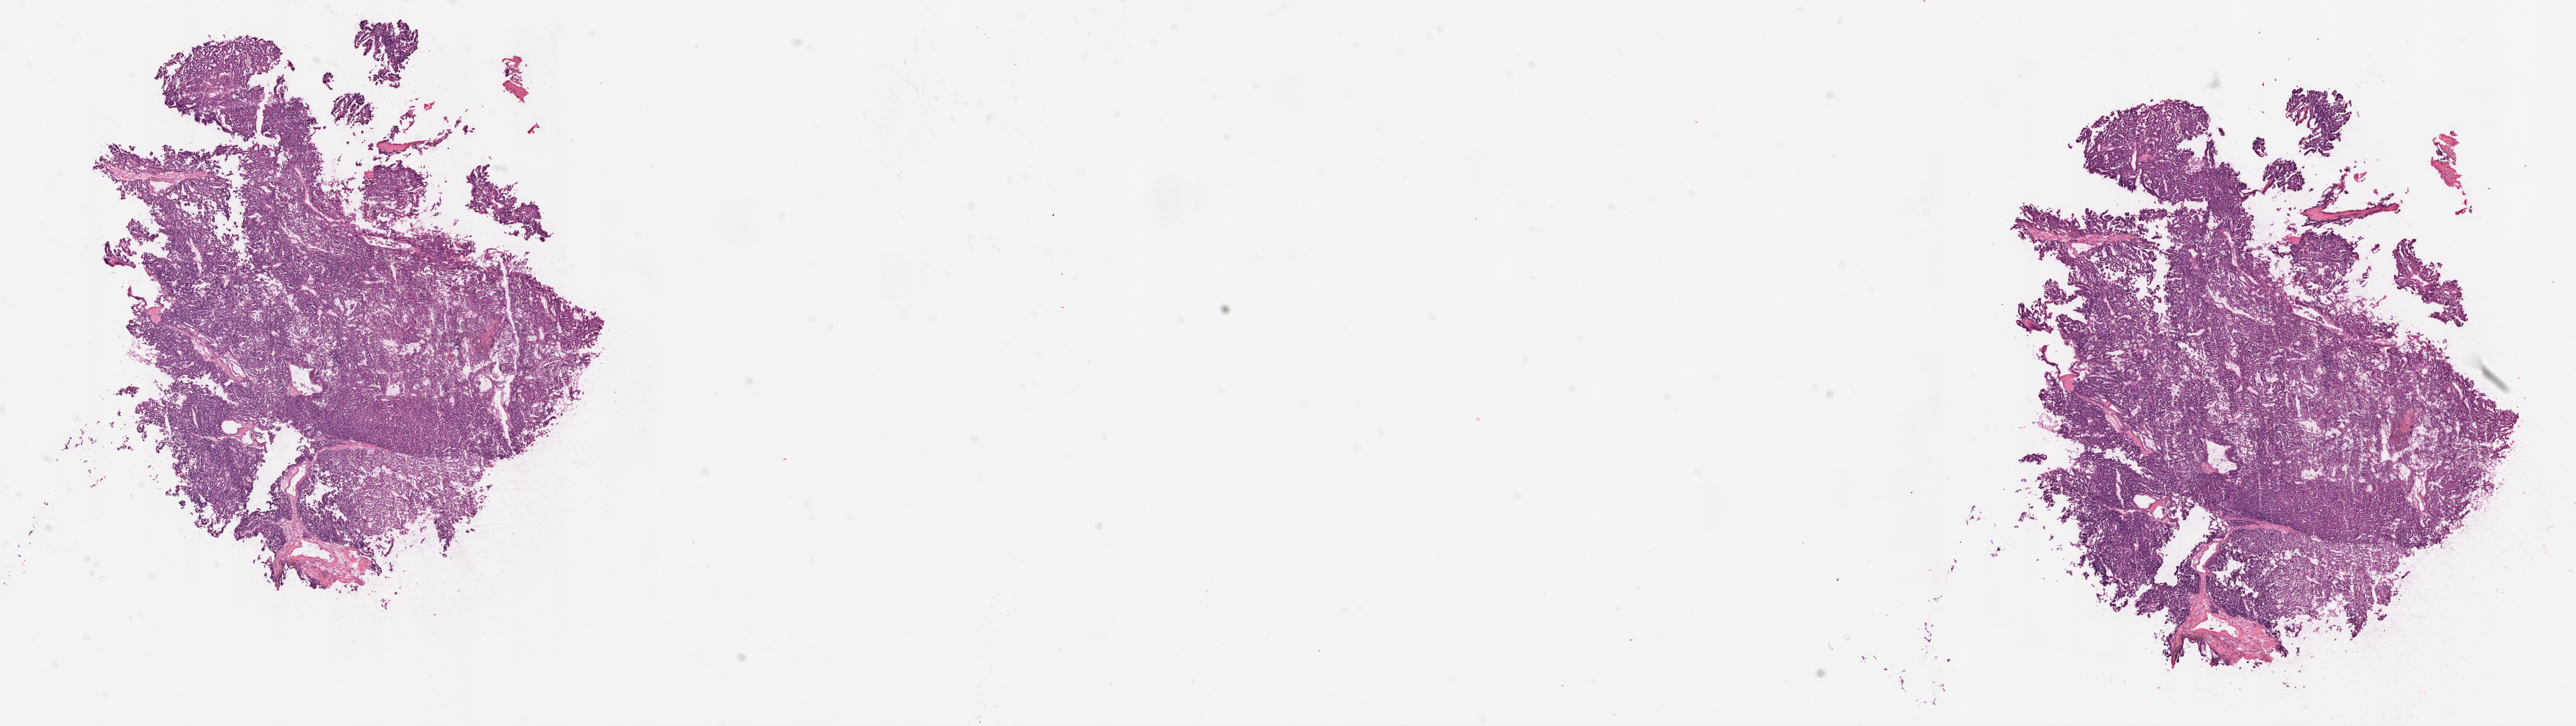
Digitized H&E-stained tissue section (whole slide) — low-resolution overview of the scanned area, about 28.1 x 7.9 mm (from a 20x scan); frozen section from the top of the tissue portion; primary tumour sample from the kidney. Female patient; age at initial diagnosis 40 years. Histologic grade: G2 (moderately differentiated). Slide review estimates, as recorded: tumour cells 90%, tumour nuclei 85%, normal cells 0%, stromal cells 10%, necrosis 0%.
AJCC pathologic stage: I. Pathologic diagnosis: Clear cell adenocarcinoma, NOS.